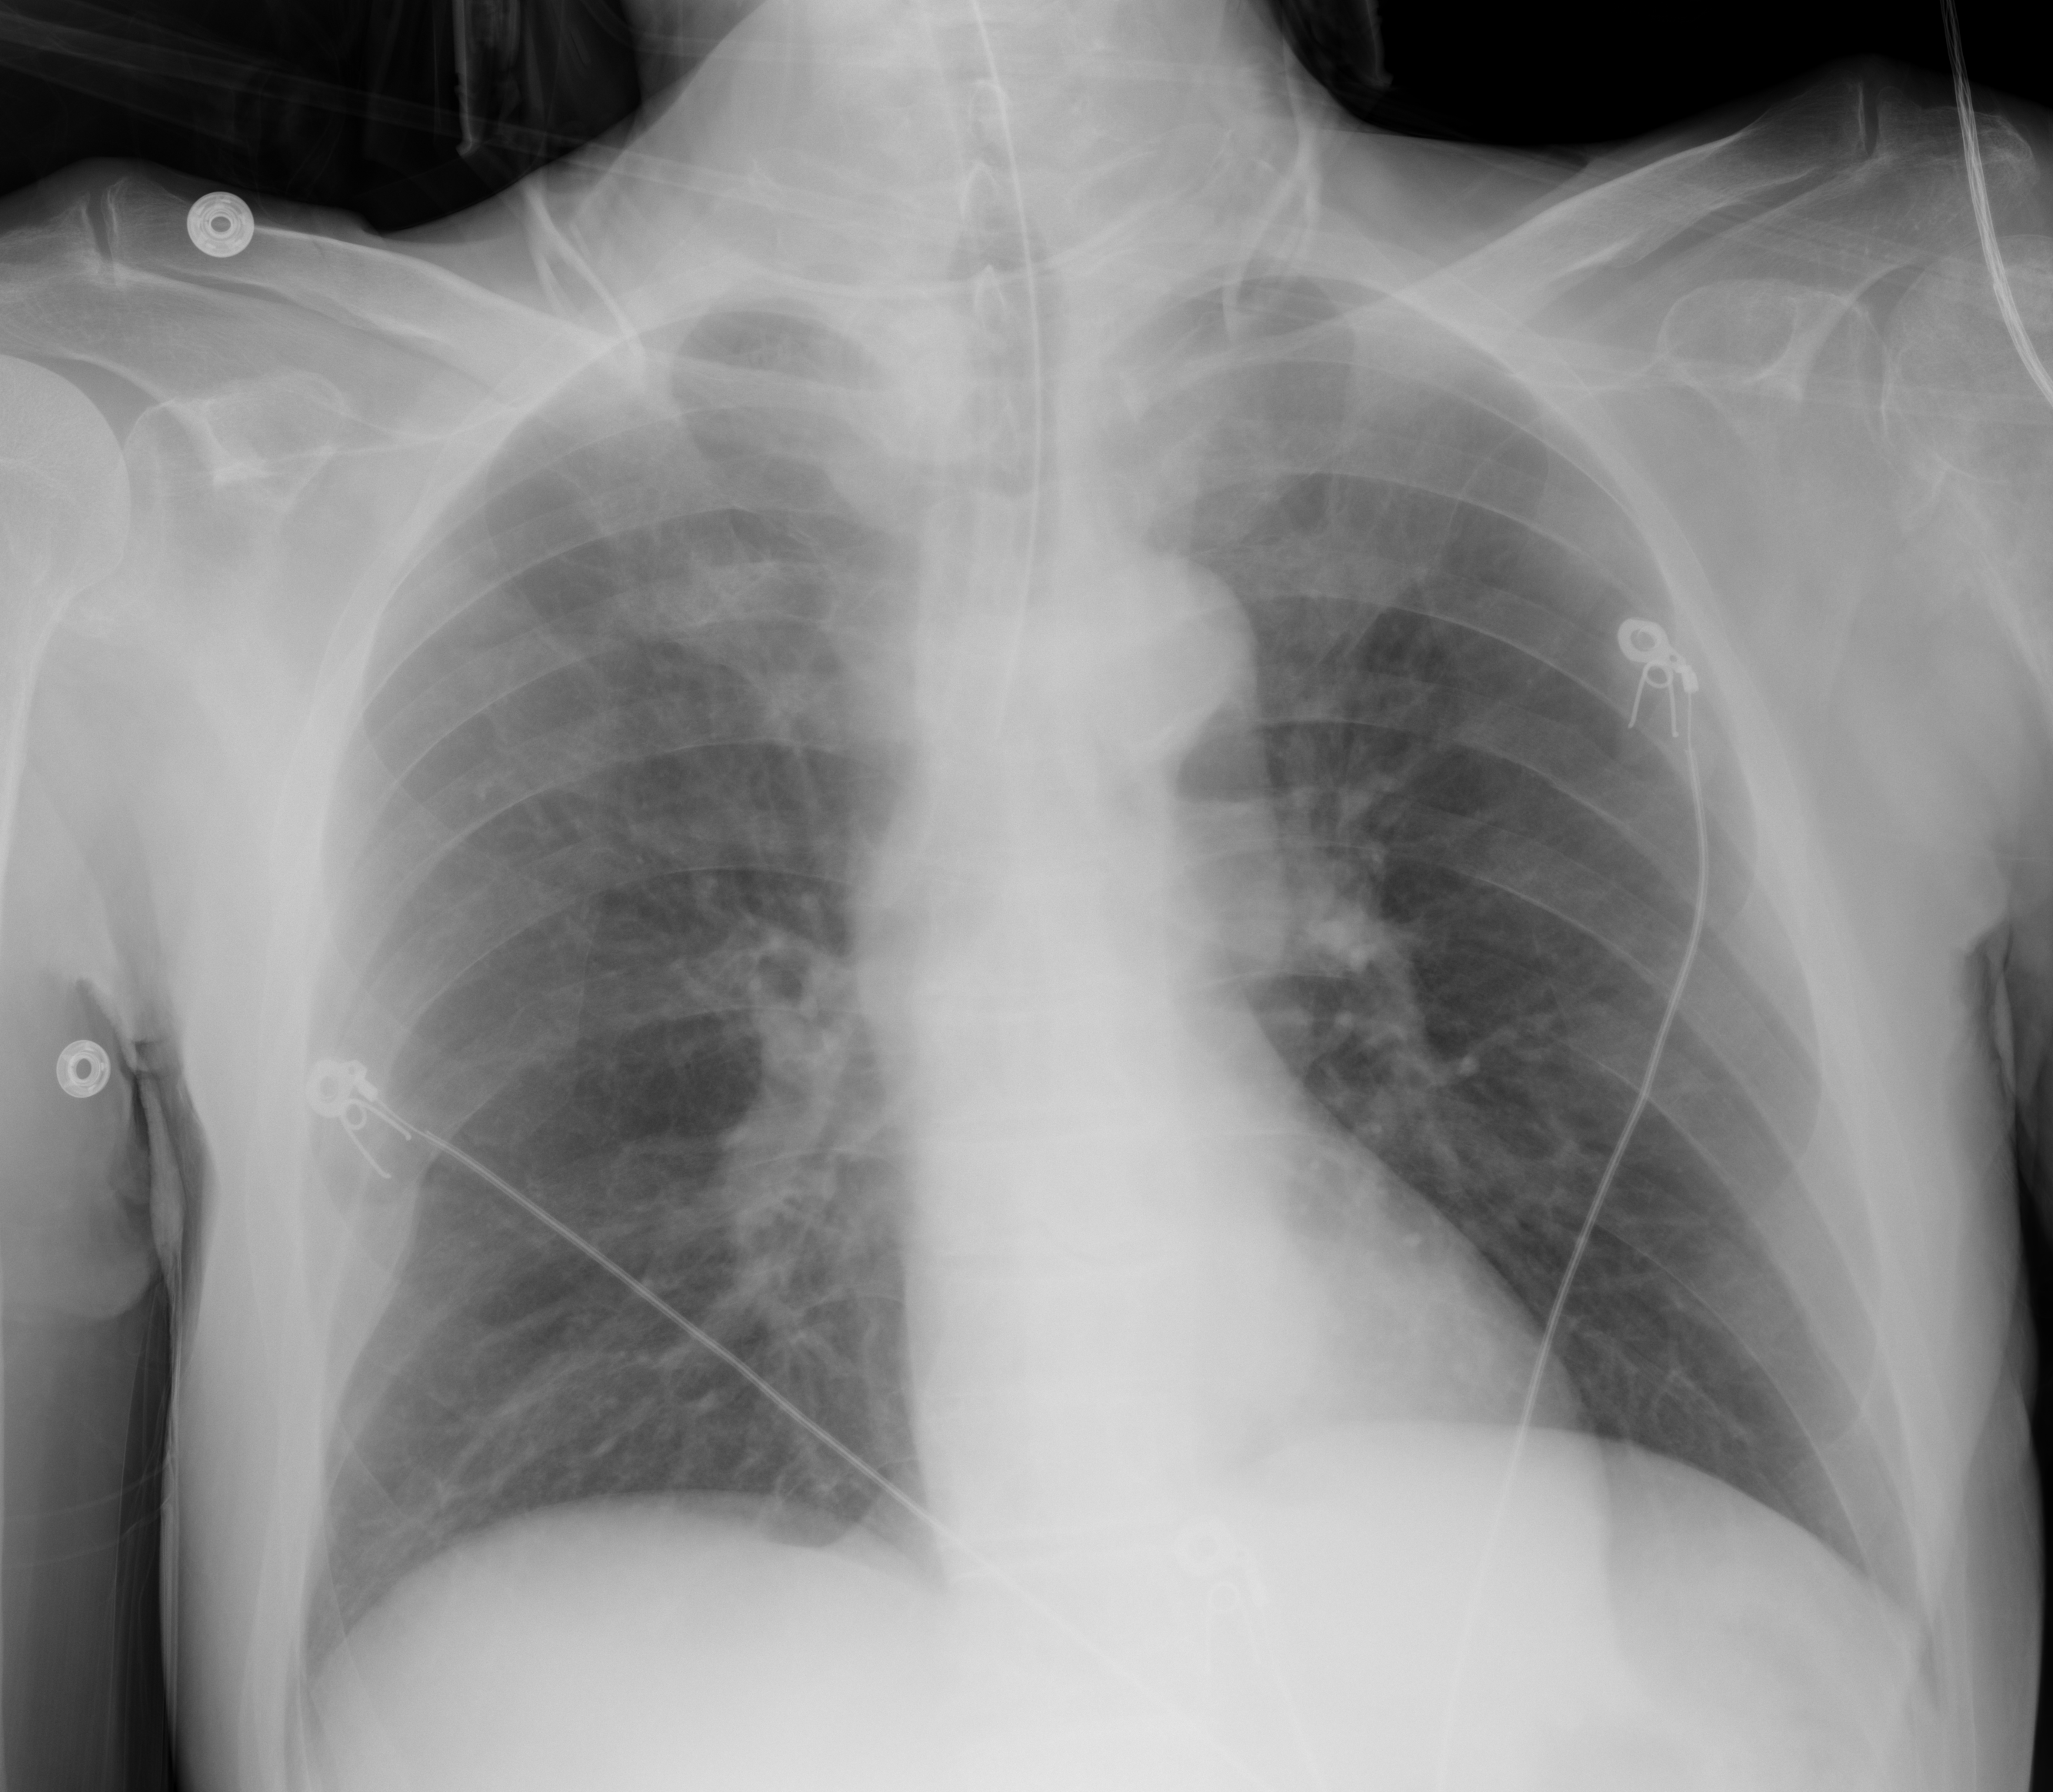
Chest X-ray (portable), AP projection. Male patient, age 59 years; imaged 0 days after the COVID-19 diagnosis.
Radiologist's key findings for this exam: The lungs appear clear with no evidence of airspace consolidation.